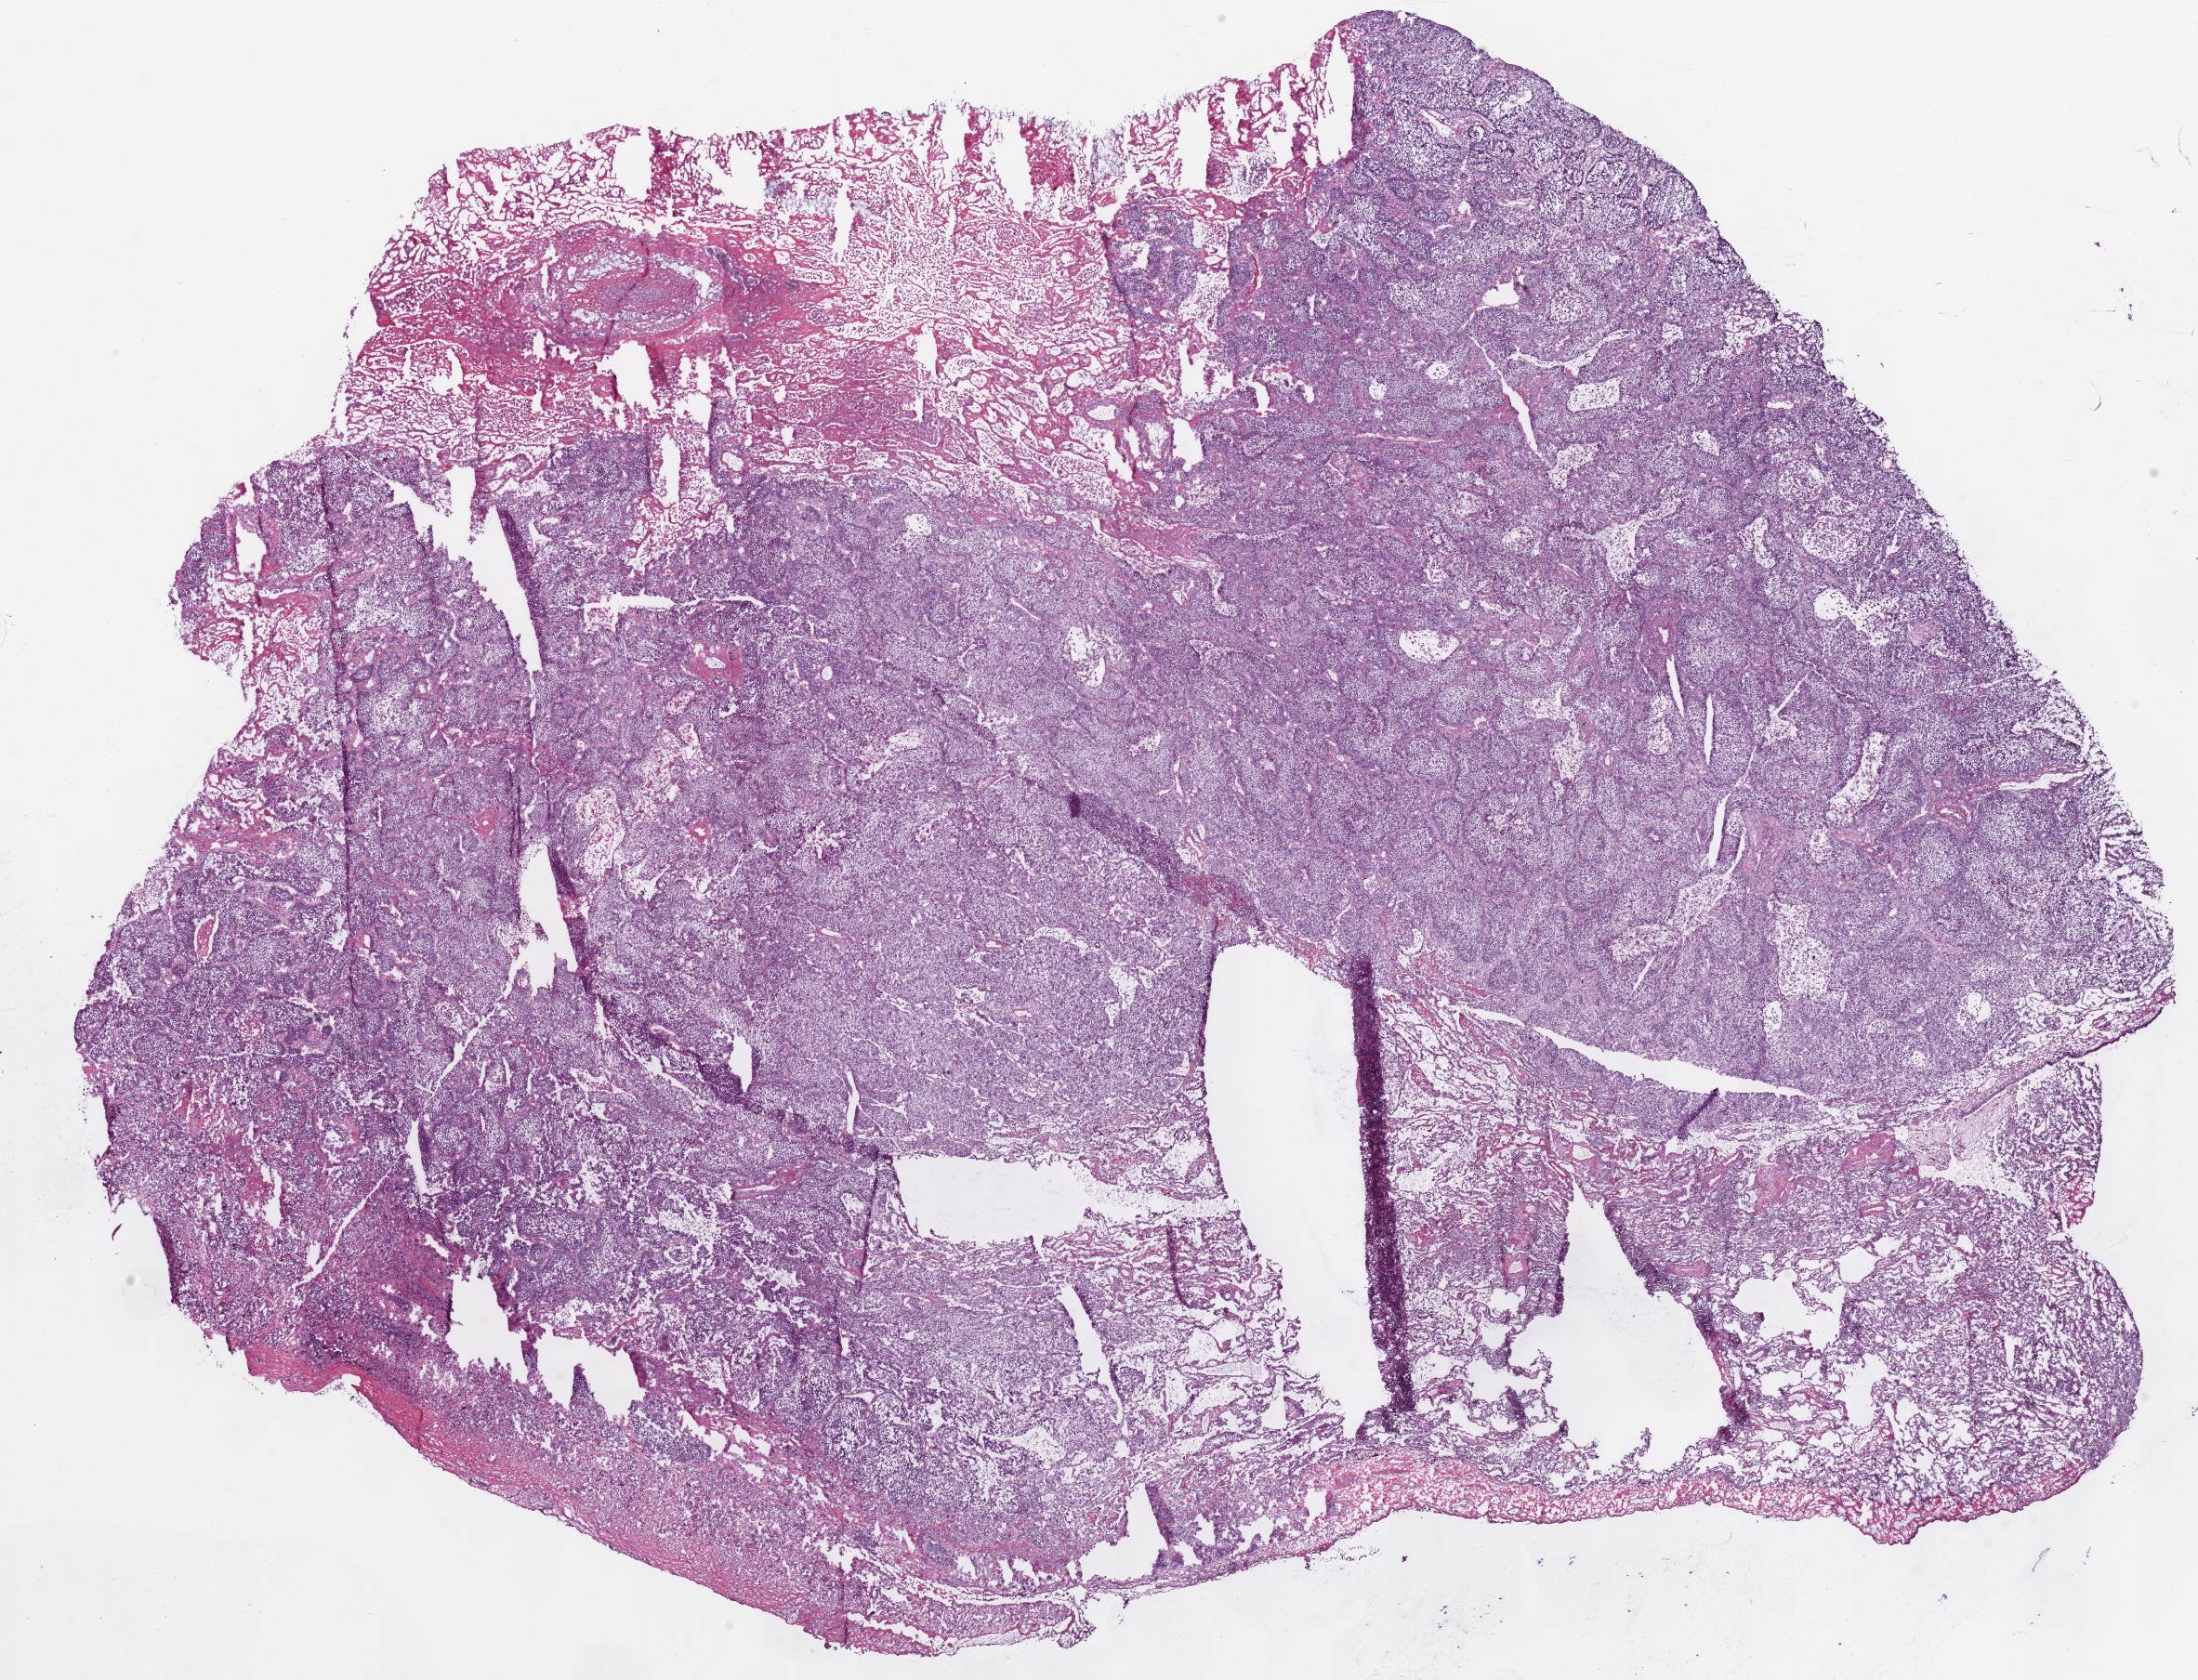
H&E whole-slide image — shown as a low-resolution overview of the whole scanned area (about 18.6 x 14.2 mm, slide scanned at 40x), frozen section, primary tumour sample from the lung. Patient: male, age at initial diagnosis 72 years. Slide review estimates, as recorded: tumour cells 70%, tumour nuclei 75%.
Diagnosis: Squamous cell carcinoma, NOS.